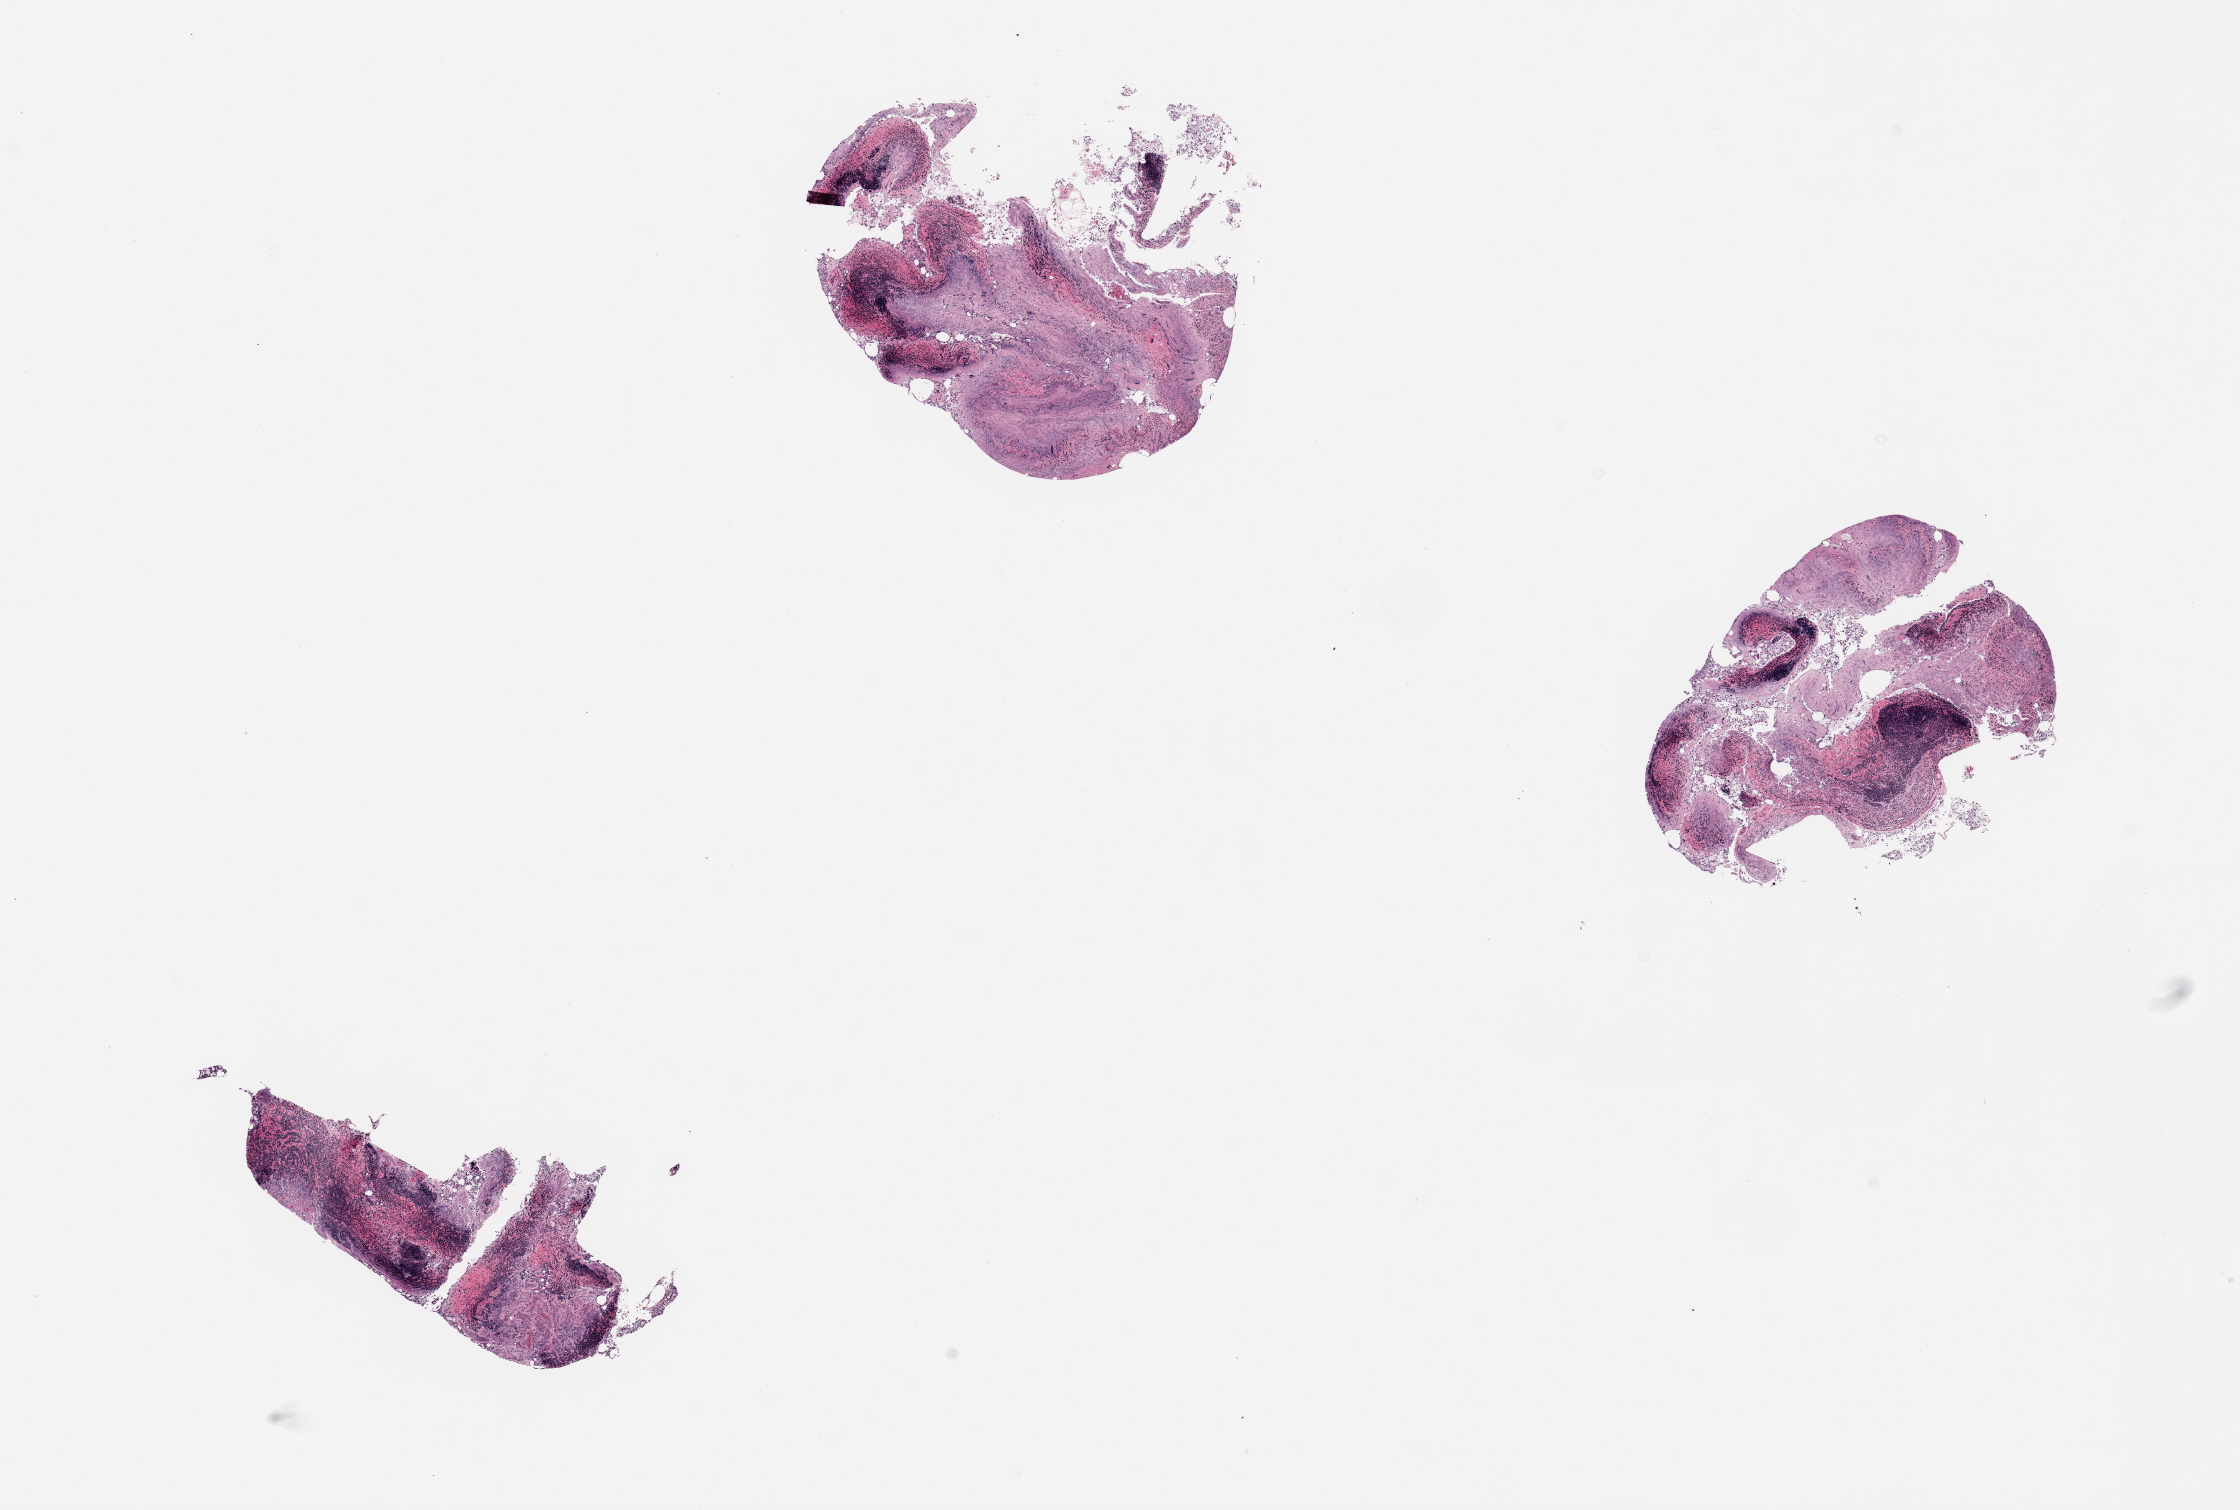
Haematoxylin and eosin whole-slide image, brightfield, shown as a low-resolution overview of the whole scanned area (about 17.7 x 11.9 mm). PAXgene-fixed, paraffin-embedded tissue. Target tissue: ileum. Donor tissue sample.
• review note (as recorded): 3 pieces, mucosa autolyzed, residual target lymphoid aggregates are ~20% of tissue